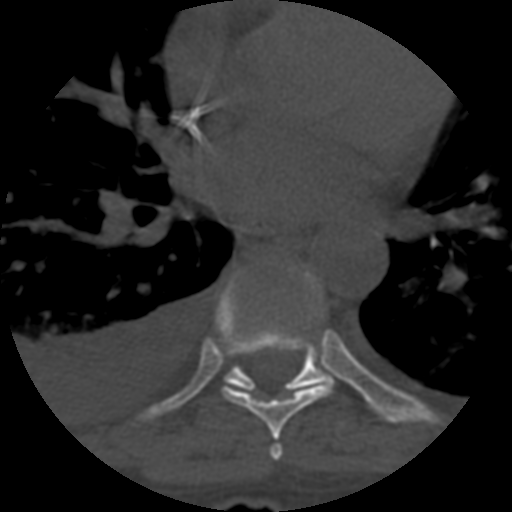
CT including the spine, one axial slice; position 408 of 708 along the scan axis; 120 kVp; one of 3 acquisitions stored at this slice position; bone window (W 1800 / L 400 HU); 1.25 mm slice thickness; 512 × 512 image matrix, field of view 160 × 160 mm. Patient age 55 years. Case-level facts recorded for this patient, not image findings: primary cancer: colon.
Structures marked on this image (semi-automatic segmentation, software-assisted and operator-edited):
- T6 vertebra: bounding box [x1, y1, x2, y2] px = [269, 444, 284, 461]
- T7 vertebra: [218, 275, 334, 440]
- T8 vertebra: [224, 272, 328, 395]